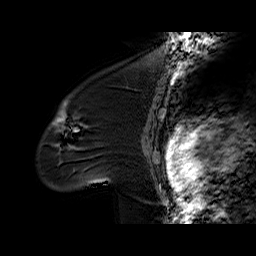
Breast MRI (dynamic contrast-enhanced), one sagittal slice. Position 46 of 60 along the scan axis. Dynamic contrast-enhanced series, time point 2 of 6 at this slice position (early post-contrast). 1.5 T. TE 6.2 ms, TR 32.4 ms. 4 mm slice thickness. 256 × 256 image matrix, field of view 200 × 200 mm. Female patient. Case-level facts recorded for this patient, not image findings: setting: breast cancer imaged before/during neoadjuvant chemotherapy; receptor status: triple-negative.
Outlined on this slice (semi-automatically segmented with operator editing):
- analysis volume of interest (the breast-tissue region the enhancement analysis was run in; not a lesion): box from (x=37, y=97) to (x=134, y=191) px
- tumour enhancement mask (voxels above the 100 % enhancement threshold inside the analysis volume of interest): (x=53, y=102)–(x=77, y=150)